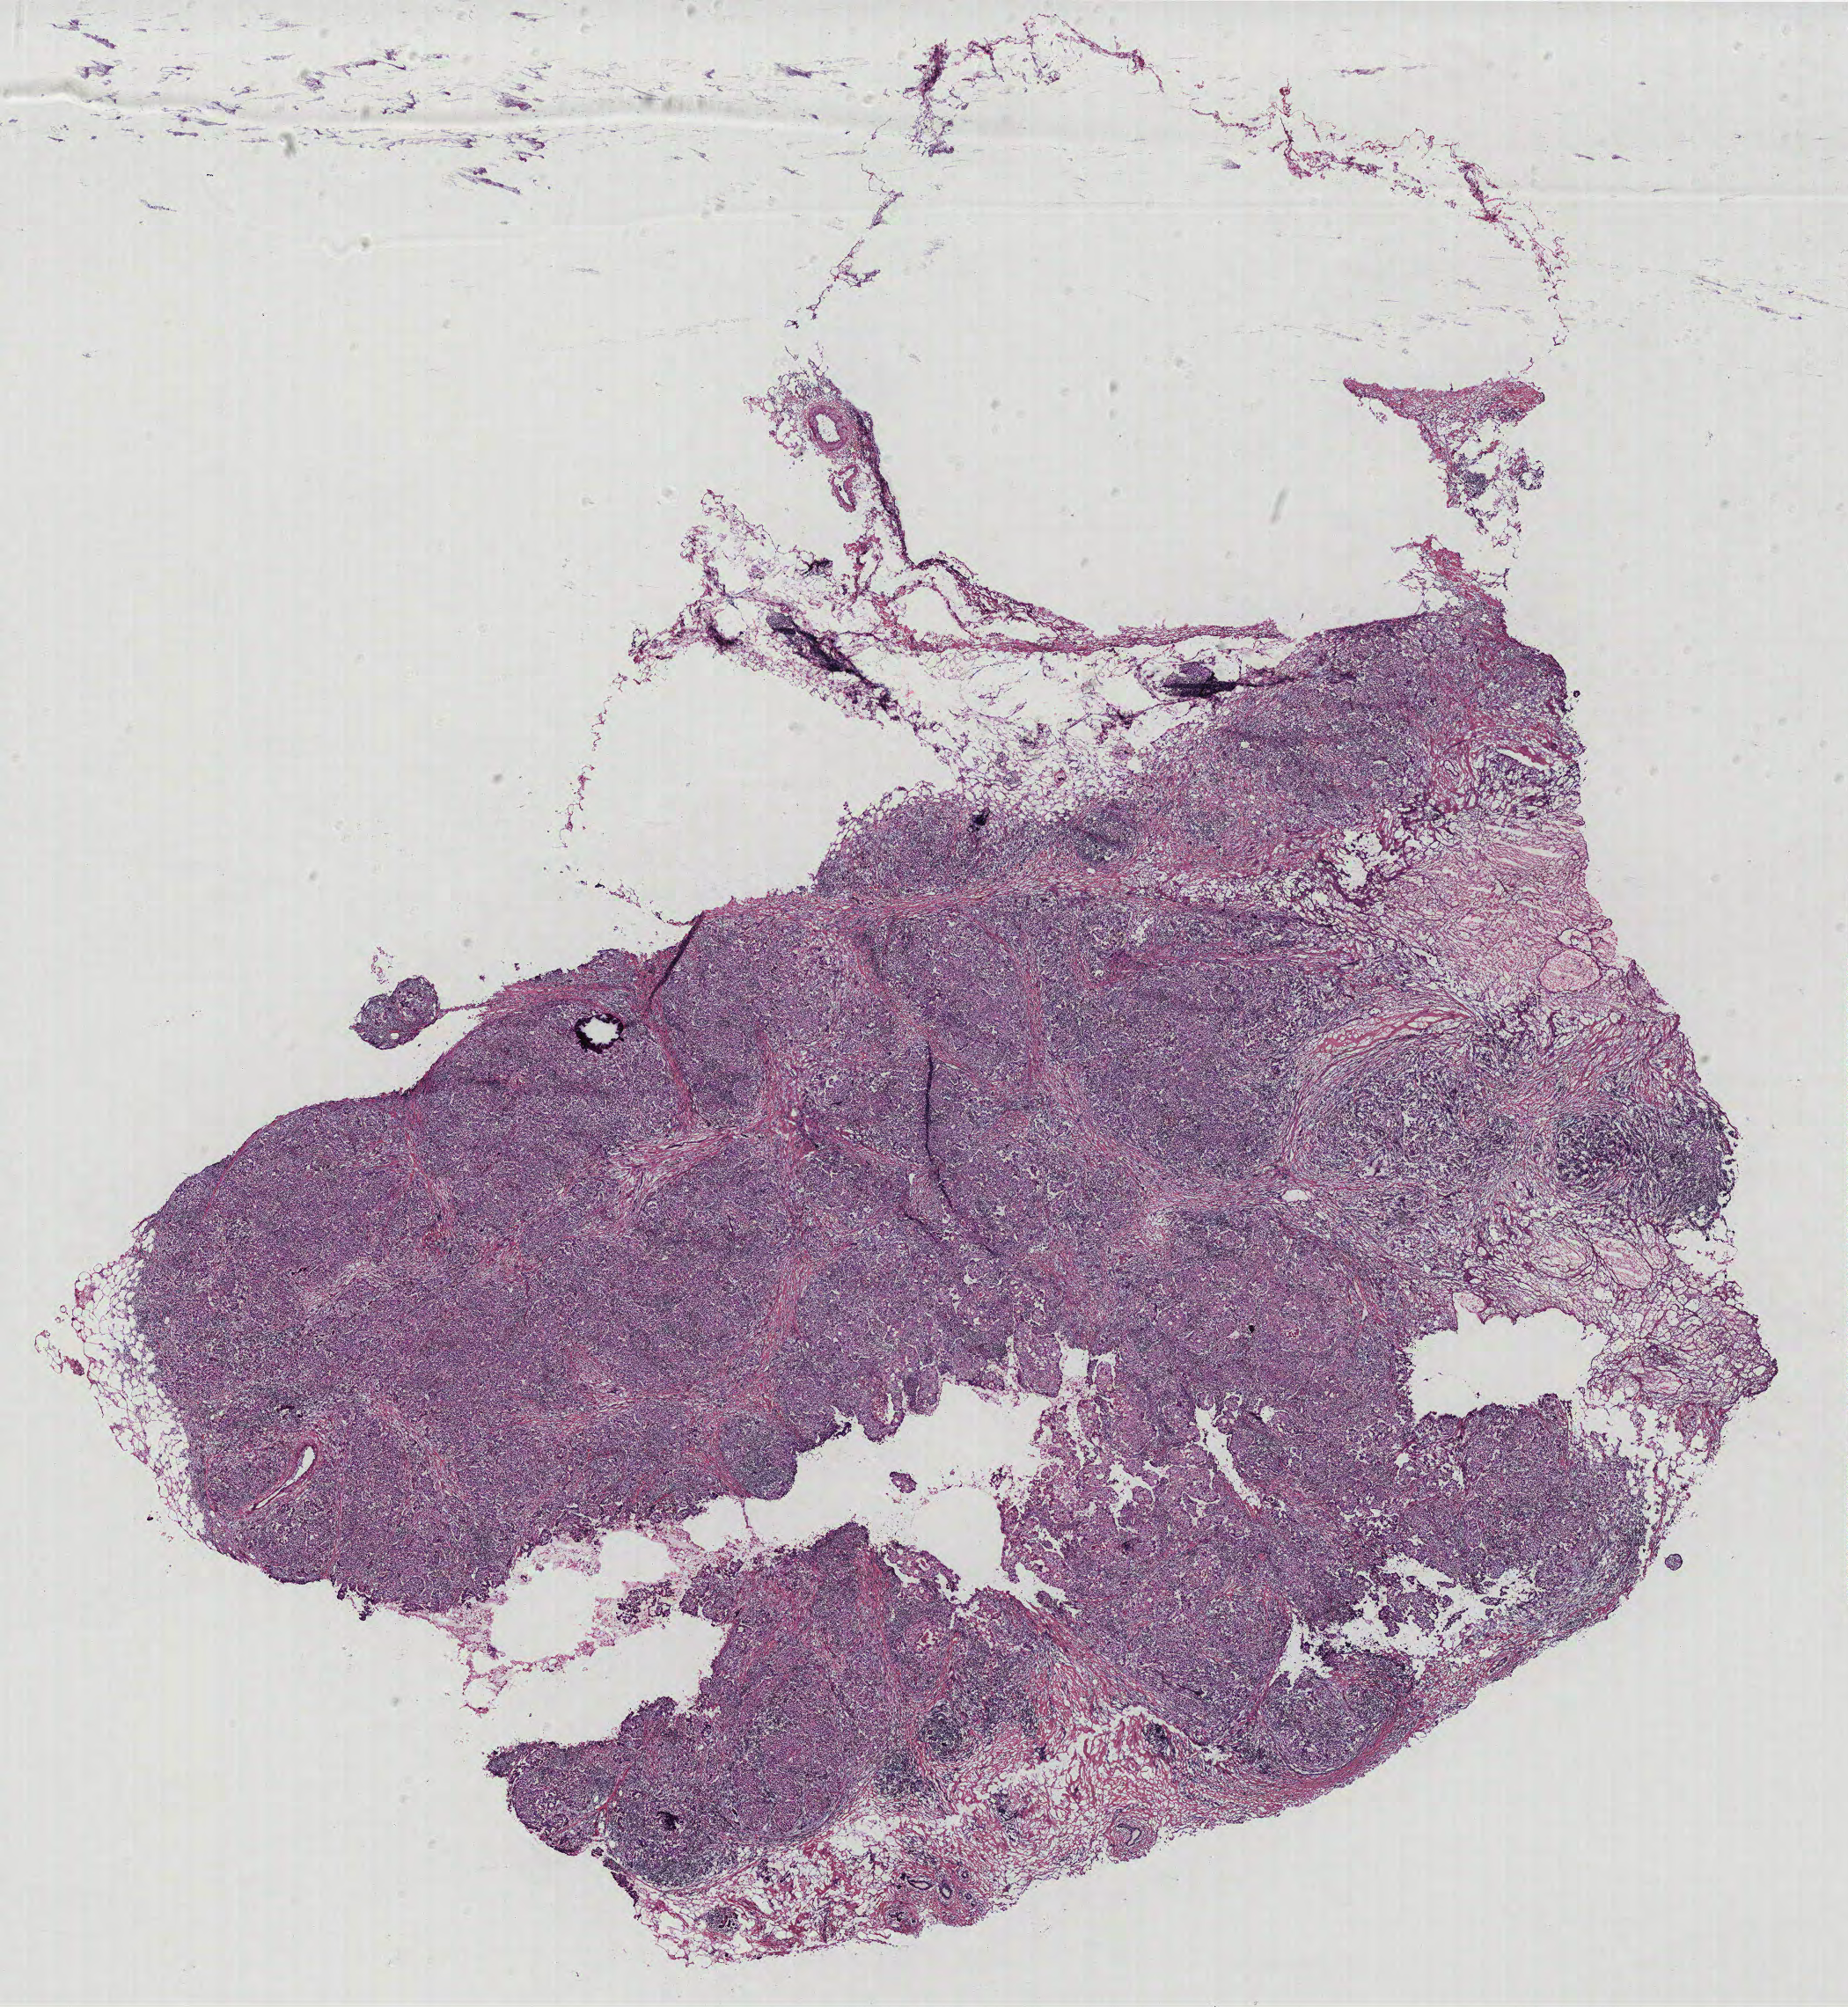
Whole-slide histology image, H&E, a low-resolution overview of the entire scanned area, about 16.8 x 18.3 mm (from a 40x scan). Breast, tissue type not recorded. Female, 50 y/o.
* patient diagnosis: Infiltrating duct carcinoma, NOS